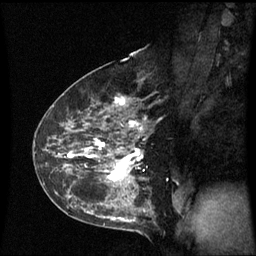
Breast MRI (dynamic contrast-enhanced), one sagittal slice. Position 37 of 60 along the scan axis. Dynamic contrast-enhanced series, image 2 of 3 at this slice position (ordered by acquisition). 1.5 T. TE 4.2 ms, TR 8.9 ms. 2.3 mm slice thickness. 256 × 256 image matrix, field of view 210 × 210 mm. Patient: female, 43 years. Case-level facts recorded for this patient, not image findings: setting: breast cancer imaged before/during neoadjuvant chemotherapy; receptor status: HER2-positive.
Outlined on this slice (semi-automatically segmented with operator editing):
- analysis volume of interest (the breast-tissue region the enhancement analysis was run in; not a lesion): bounding box (x1, y1, x2, y2) in pixels: (56, 80, 154, 195)
- tumour enhancement mask (voxels above the 70 % enhancement threshold inside the analysis volume of interest): (68, 97, 144, 182)